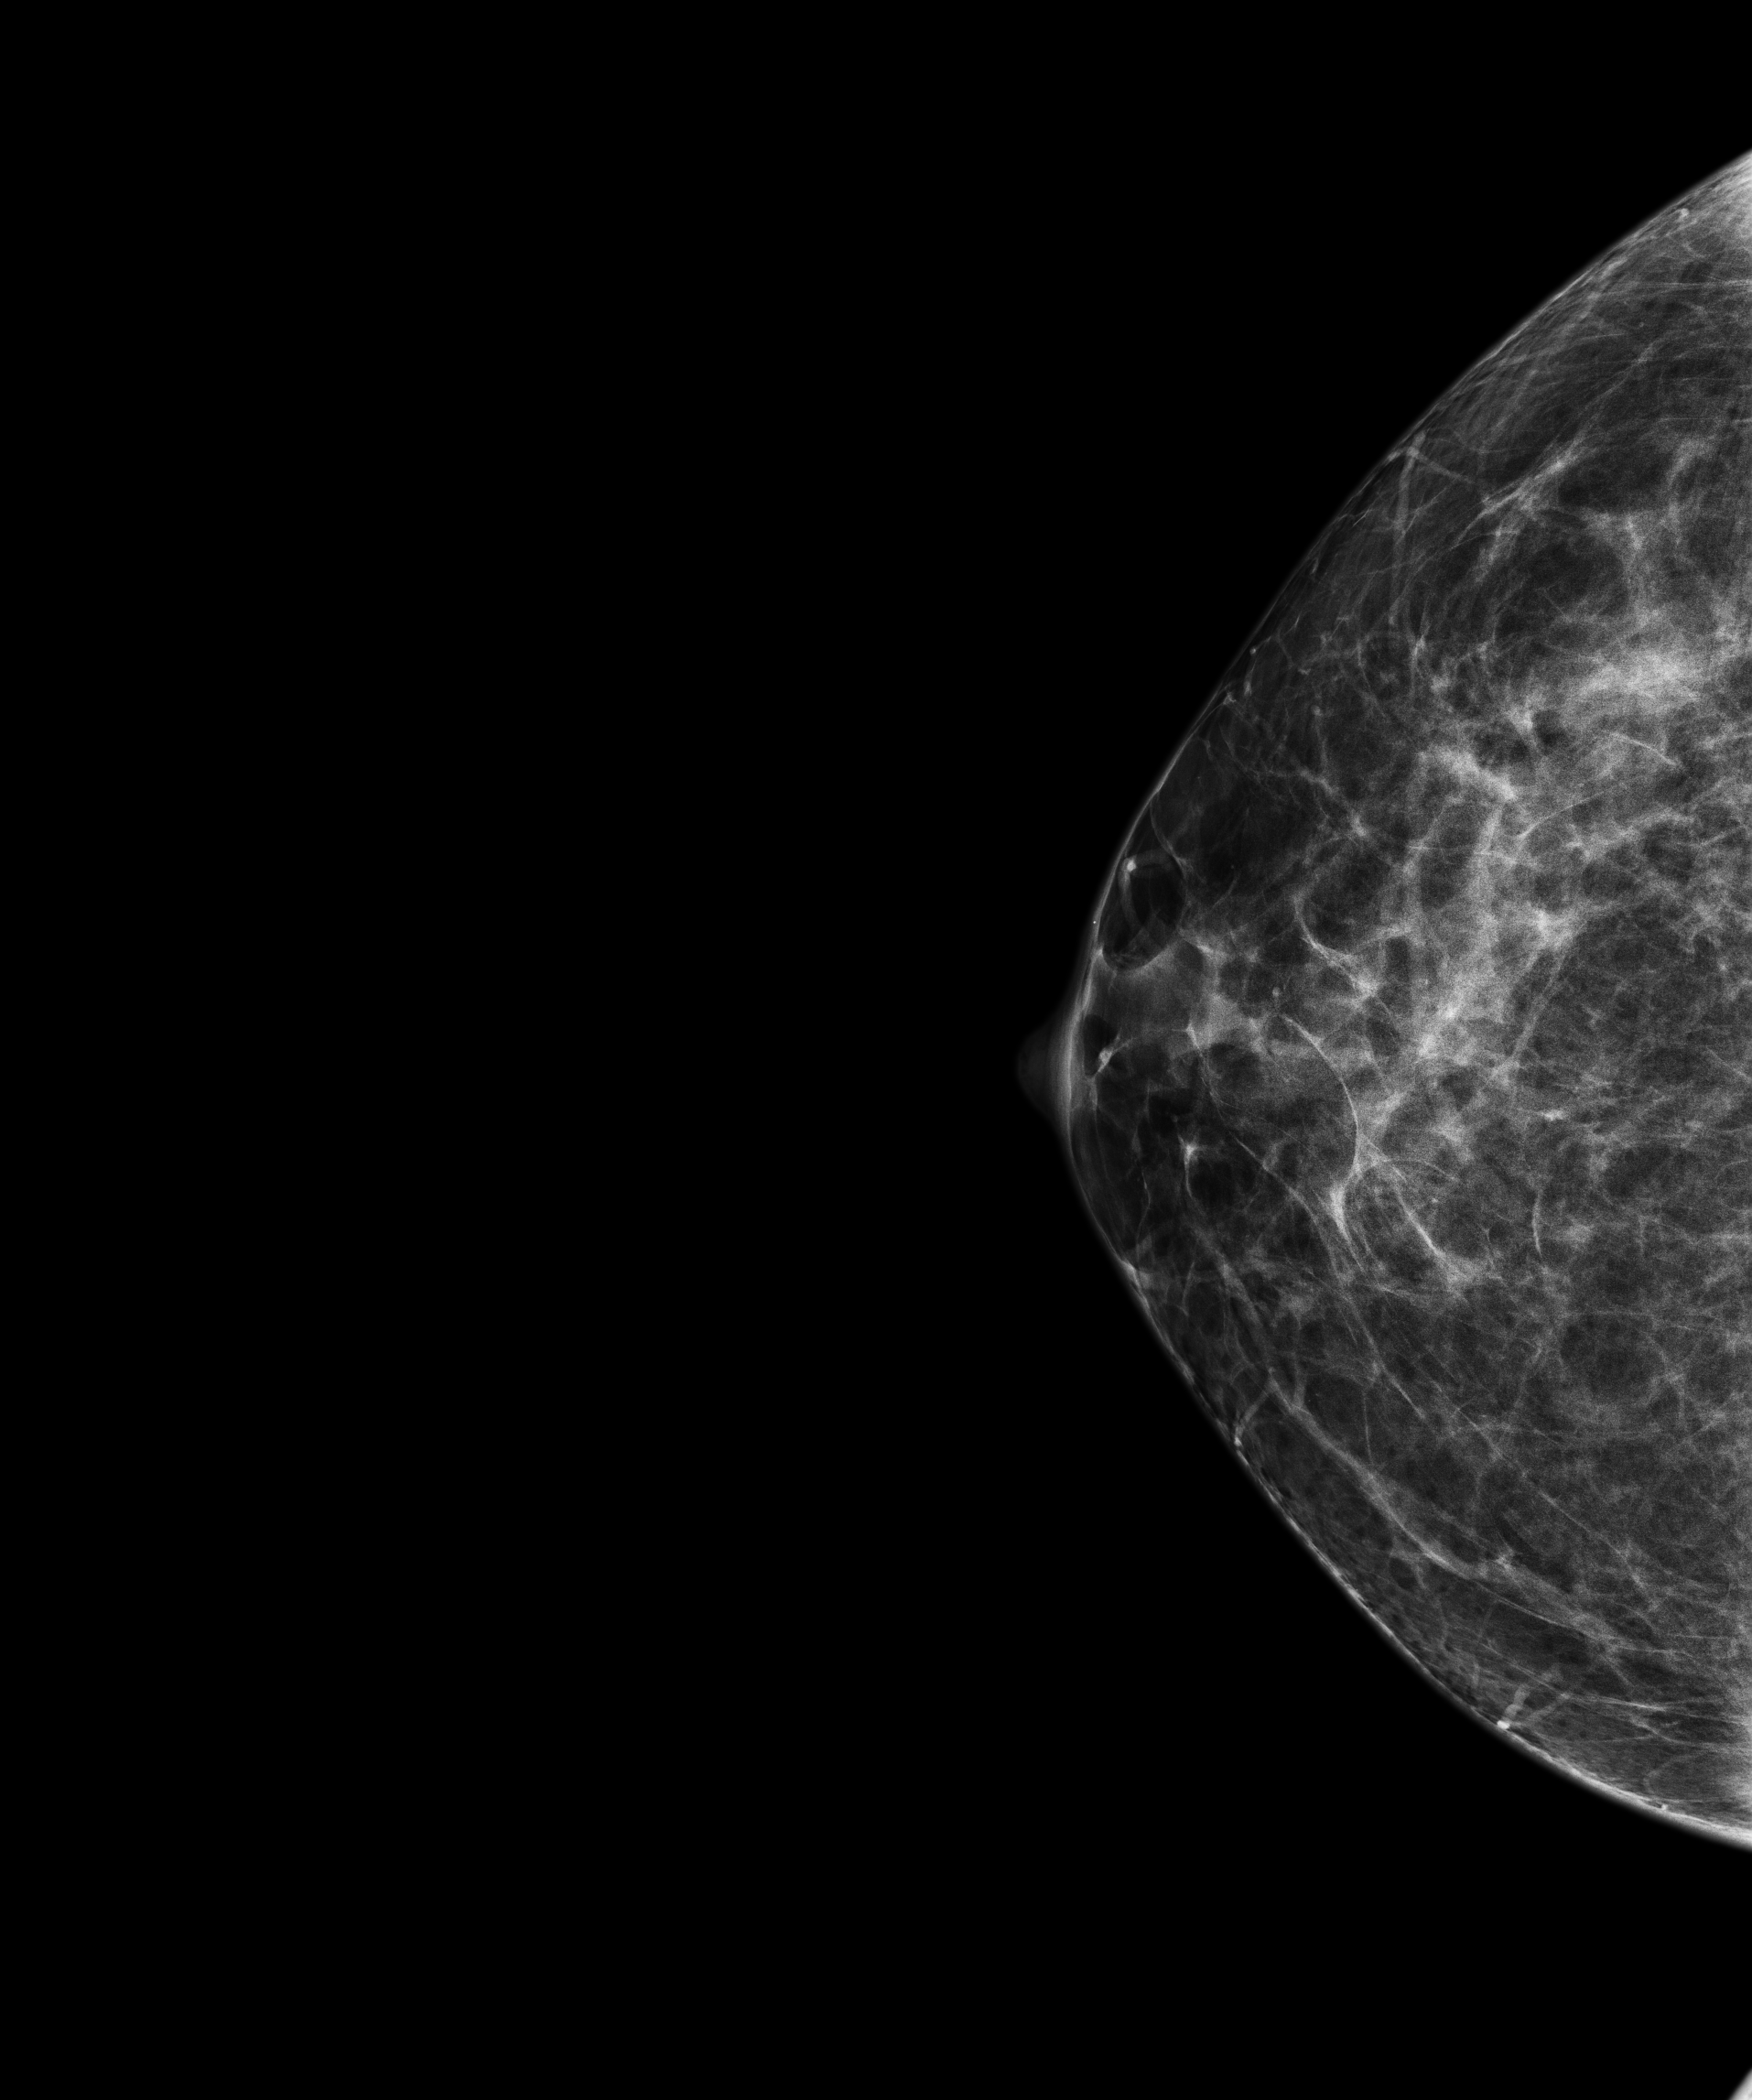
Annual screening mammography examination; compressed breast thickness 63.9 mm; system: Senographe Pristina. Patient: female, 43 years.
Image type: full-field digital mammogram. Breast: right. Projection: cranio-caudal projection.